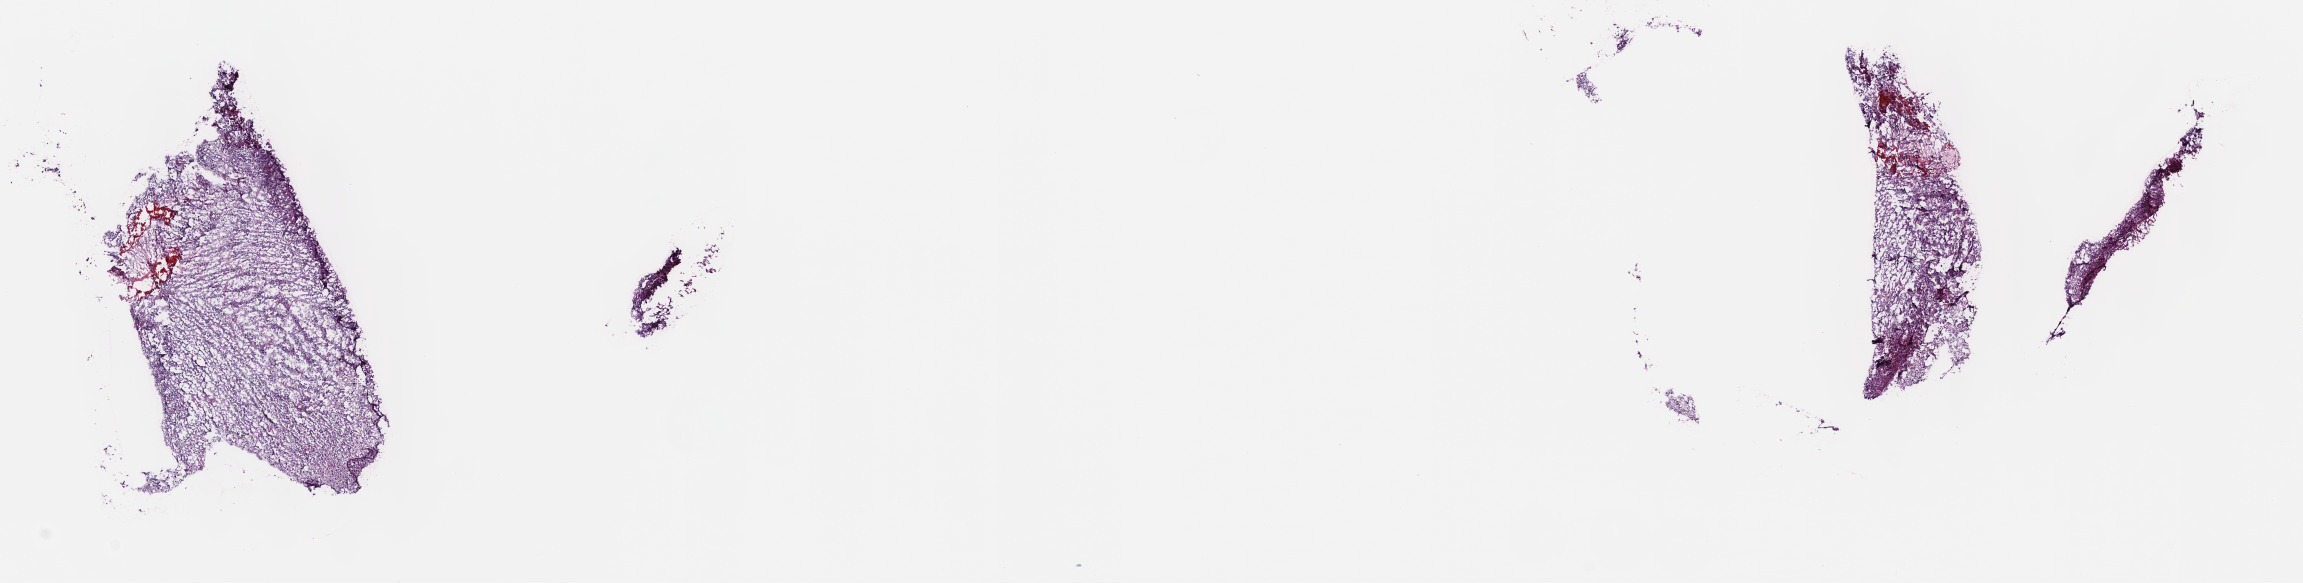
H&E-stained whole-slide image — a low-resolution overview of the entire scanned area, about 18.6 x 4.7 mm (slide scanned at 40x), frozen section from the top of the tissue portion, brain, primary tumour sample. Male, age 25 years at initial diagnosis. Histologic grade: G3 (poorly differentiated). Pathologist review of this section (percent, as recorded): tumour cells 80%, tumour nuclei 90%, normal cells 5%, stromal cells 15%, necrosis 0%. Inflammatory infiltration, as recorded: lymphocyte infiltration 0%, monocyte infiltration 0%, neutrophil infiltration 0%.
Pathologic diagnosis: Oligodendroglioma, anaplastic (cerebrum). Laterality: left.